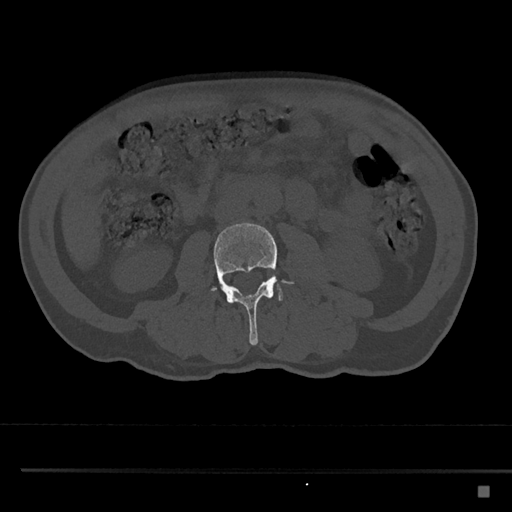
CT including the spine, one axial slice. Slice 691 of 797 in the series (ordered by position). Reconstruction kernel Br40s/3. Bone window (W 1800 / L 400 HU). 0.5 mm slice thickness. 512 × 512 image matrix, field of view 391 × 391 mm. Male patient, age 59 years. Case-level facts recorded for this patient, not image findings: primary cancer: prostate.
Structures marked on this image (semi-automatic segmentation, software-assisted and operator-edited):
- L3 vertebra: box from (x=211, y=223) to (x=294, y=345) px
- L4 vertebra: (x=277, y=279)–(x=283, y=302)